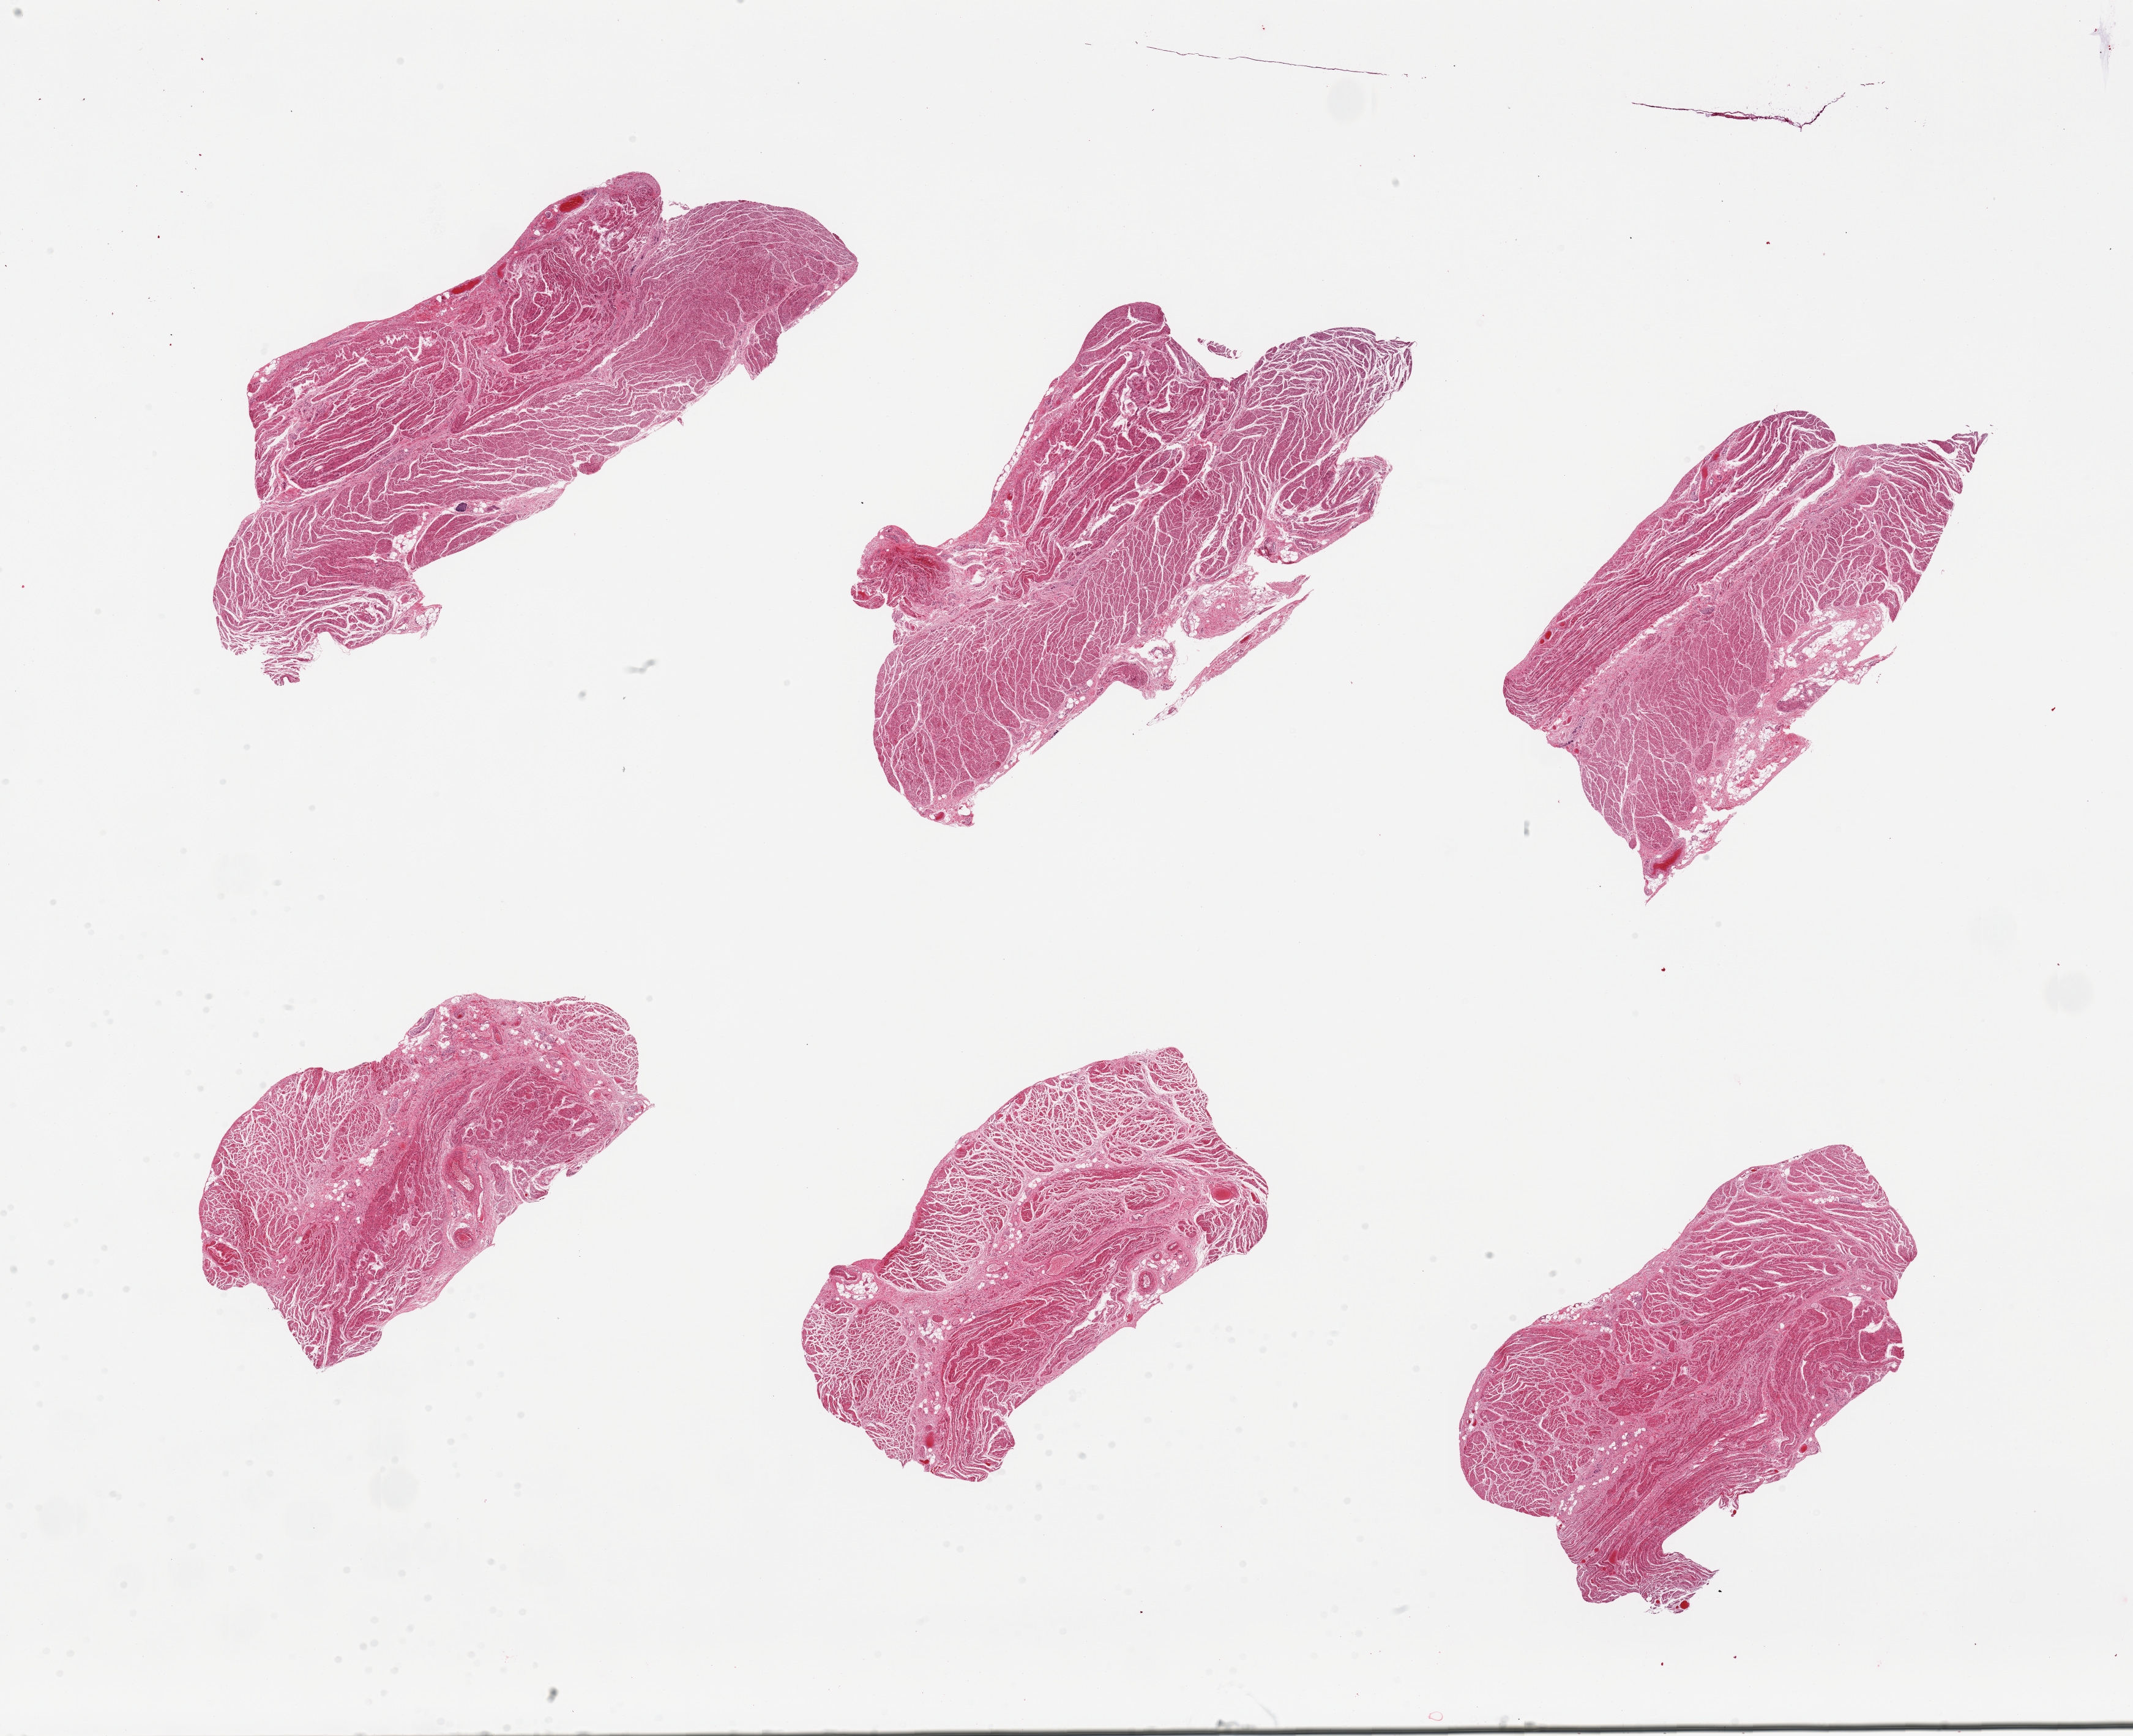
Digitized haematoxylin and eosin-stained section, low-resolution overview of the scanned area, about 27.6 x 22.4 mm (acquisition: 20x scan), PAXgene-fixed paraffin-embedded (PFPE) section, section of gastroesophageal junction (target tissue), donor tissue sample. Donor: male.
* pathologist's review note for this sample: 6 pieces; well trimmed